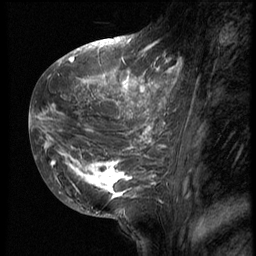
Breast MRI (dynamic contrast-enhanced), one sagittal slice. Position 21 of 62 along the scan axis. 3 images stored at this slice position (order not interpretable as contrast timing). 1.5 T. TE 4.2 ms, TR 9 ms. 256 × 256 image matrix, field of view 180 × 180 mm. Female patient, age 28 years. Case-level facts recorded for this patient, not image findings: setting: breast cancer imaged before/during neoadjuvant chemotherapy.
Structures marked on this image (semi-automatic segmentation, software-assisted and operator-edited):
- analysis volume of interest (the breast-tissue region the enhancement analysis was run in; not a lesion): box from (x=42, y=47) to (x=183, y=207) px
- tumour enhancement mask (voxels above the 140 % enhancement threshold inside the analysis volume of interest): (x=42, y=48)–(x=183, y=198)